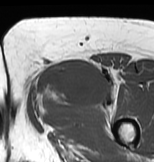
MRI of an extremity soft-tissue mass, one axial slice. Slice 39 of 83 in the series (ordered by position). MR volume resampled by the dataset authors to the PET/CT grid (not the native acquisition matrix). 154 × 162 image matrix, field of view 150 × 158 mm. Female patient. Case-level facts recorded for this patient, not image findings: histological type: myxofibrosarcoma; grade: intermediate; site of the primary tumour: left thigh.
Structures marked on this image (expert contour drawn on MRI and transferred to this co-registered scan by the dataset authors):
- gross tumour volume including surrounding oedema: box from (x=28, y=59) to (x=120, y=119) px
- gross tumour volume (mass): (x=35, y=59)–(x=107, y=108)